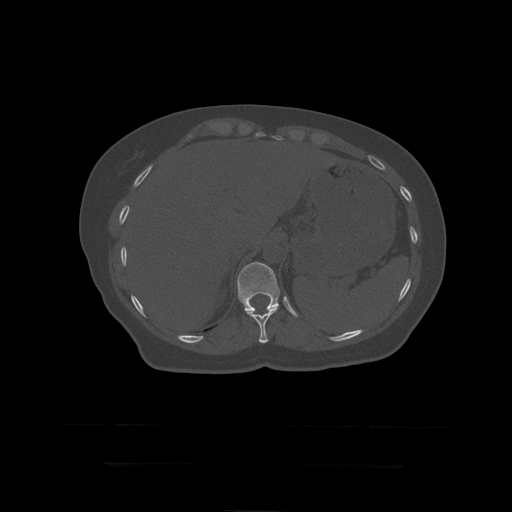
CT including the spine, one axial slice. Slice 209 of 399 in the series (ordered by position). Bone window (W 1800 / L 400 HU). 1.25 mm slice thickness. 512 × 512 image matrix, field of view 450 × 450 mm. Patient age 41 years. Case-level facts recorded for this patient, not image findings: primary cancer: breast.
Outlined on this slice (semi-automatically segmented with operator editing):
- T11 vertebra: box from (x=246, y=305) to (x=280, y=344) px
- T12 vertebra: (x=237, y=262)–(x=280, y=312)